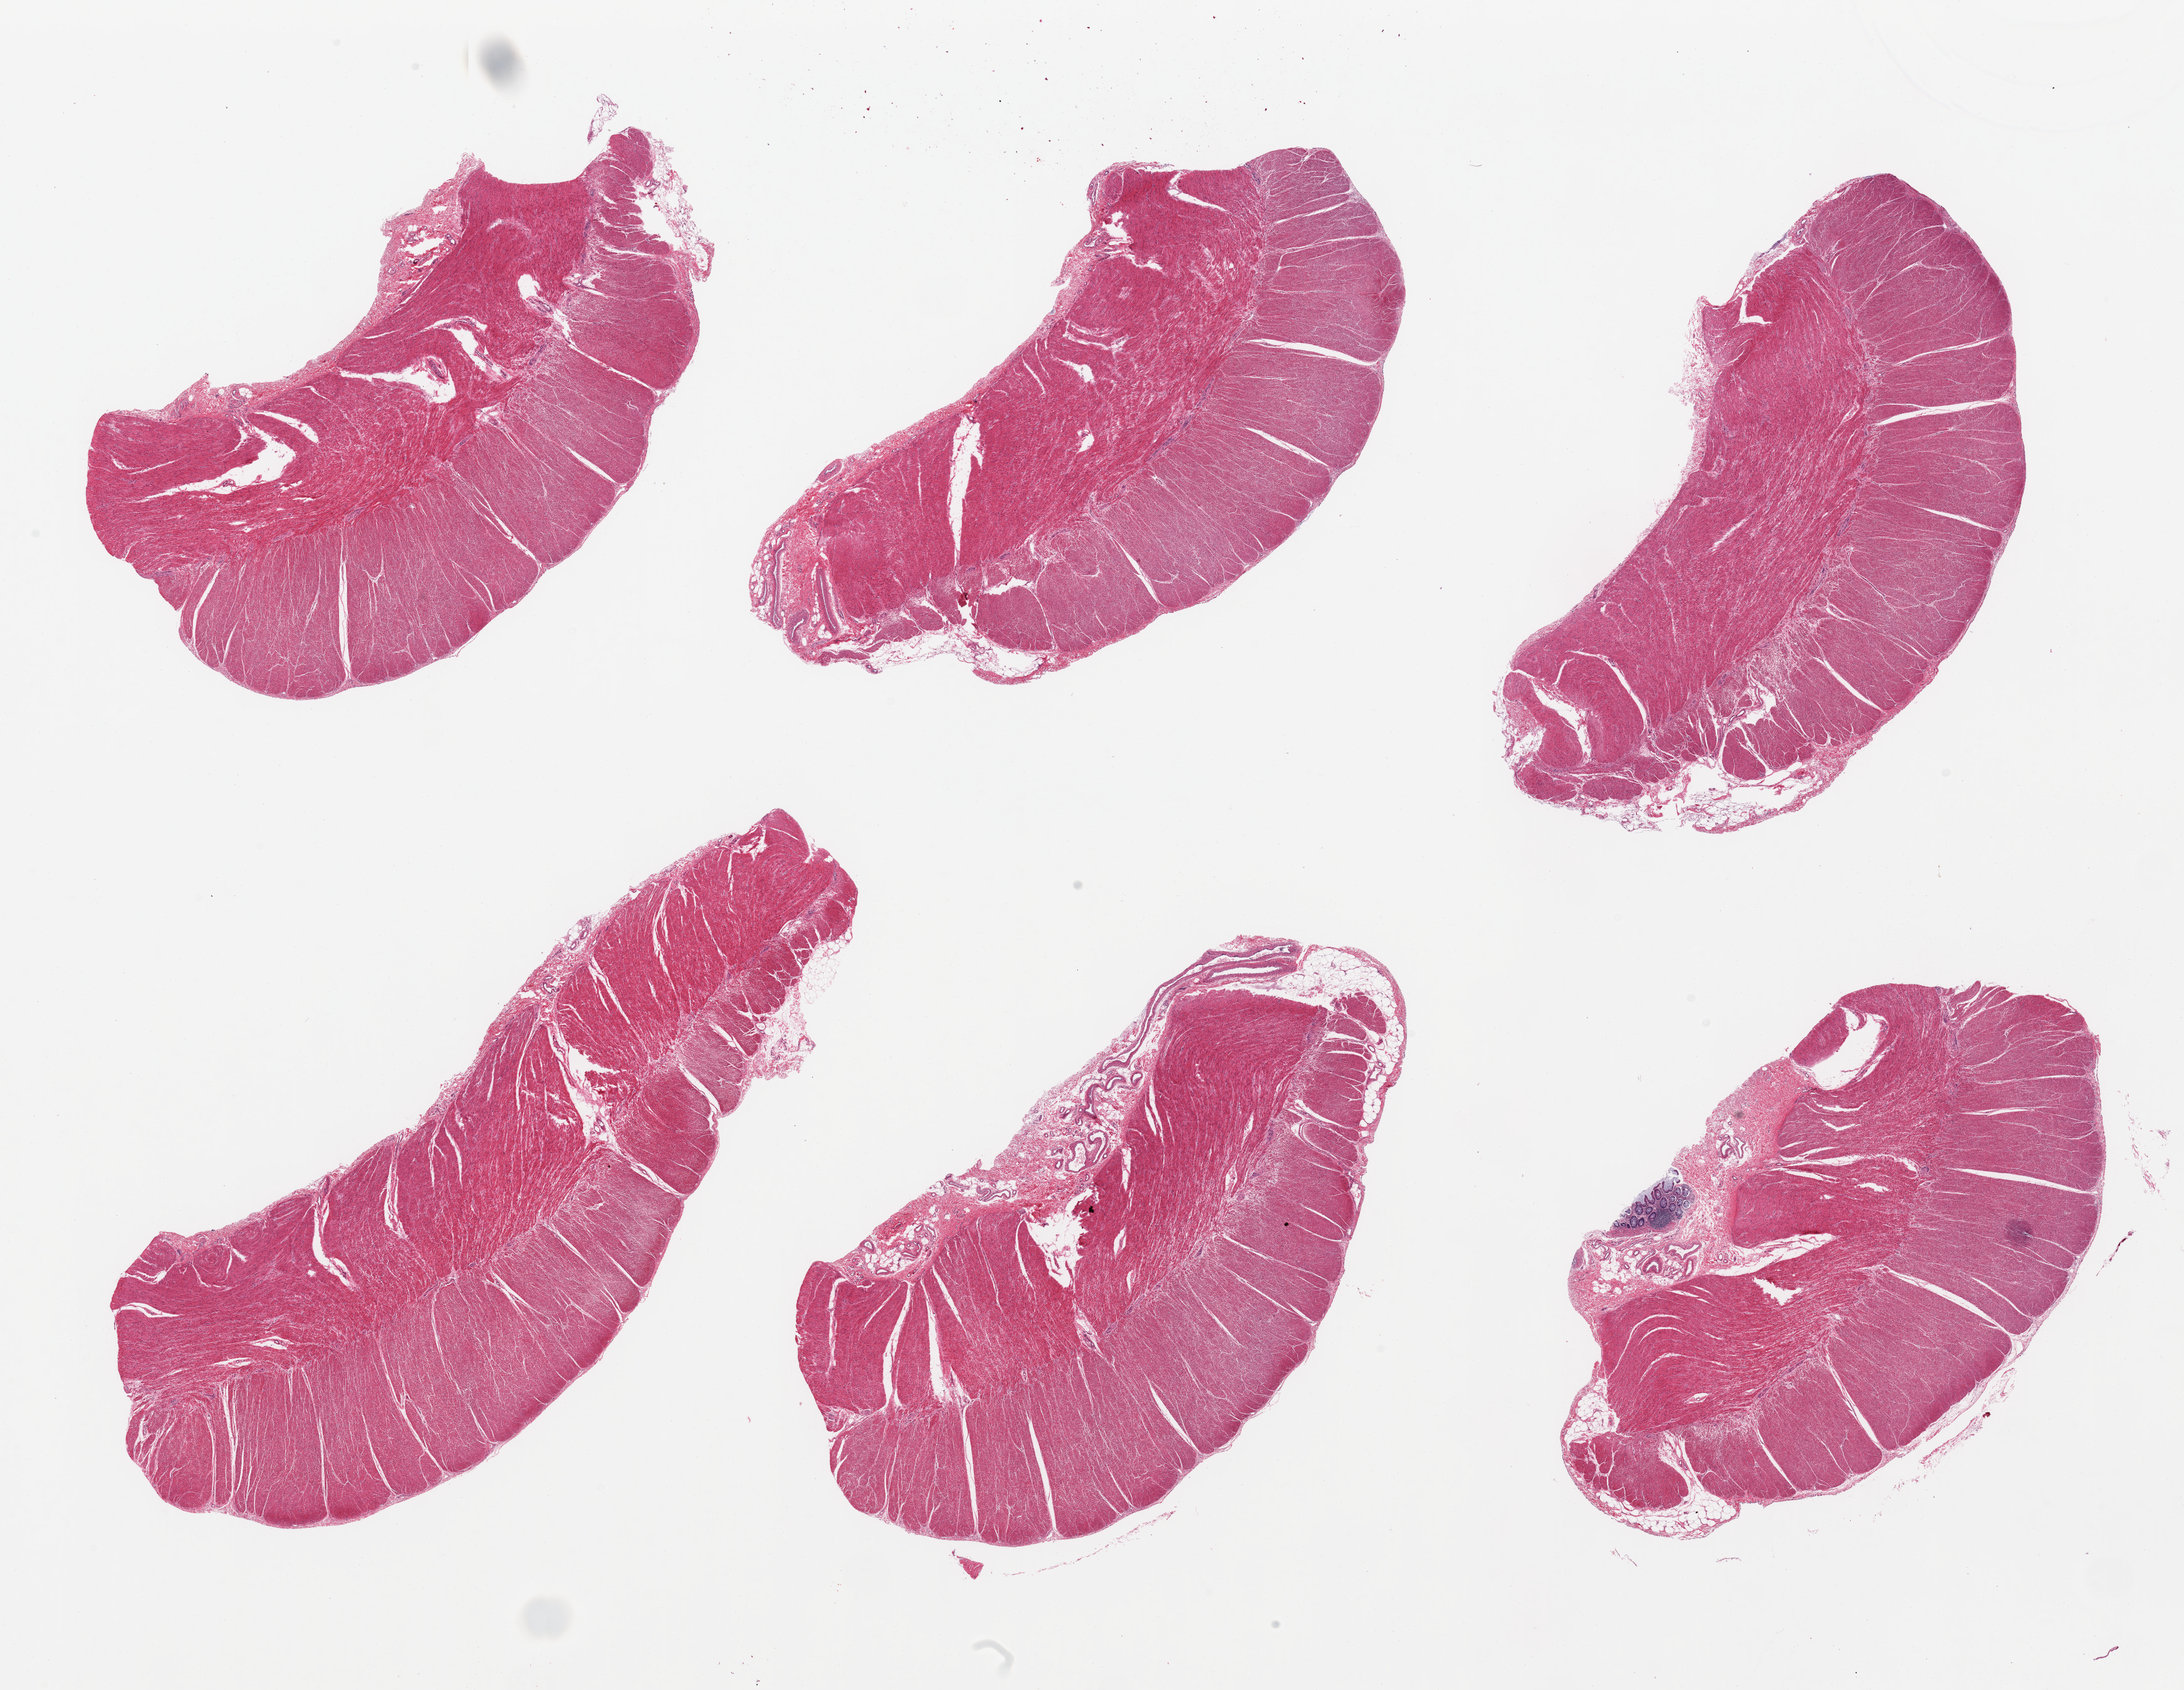
Whole-slide image, H&E stain, low-resolution overview of the scanned area, about 27.6 x 21.3 mm. PAXgene-fixed paraffin-embedded (PFPE) section. Section of sigmoid colon (target tissue). Tissue donor sample. Donor: male.
Pathologist's review note for this sample: 6 pieces; target muscularis with small portion of residual submucosa/mucosa in 1 piece.